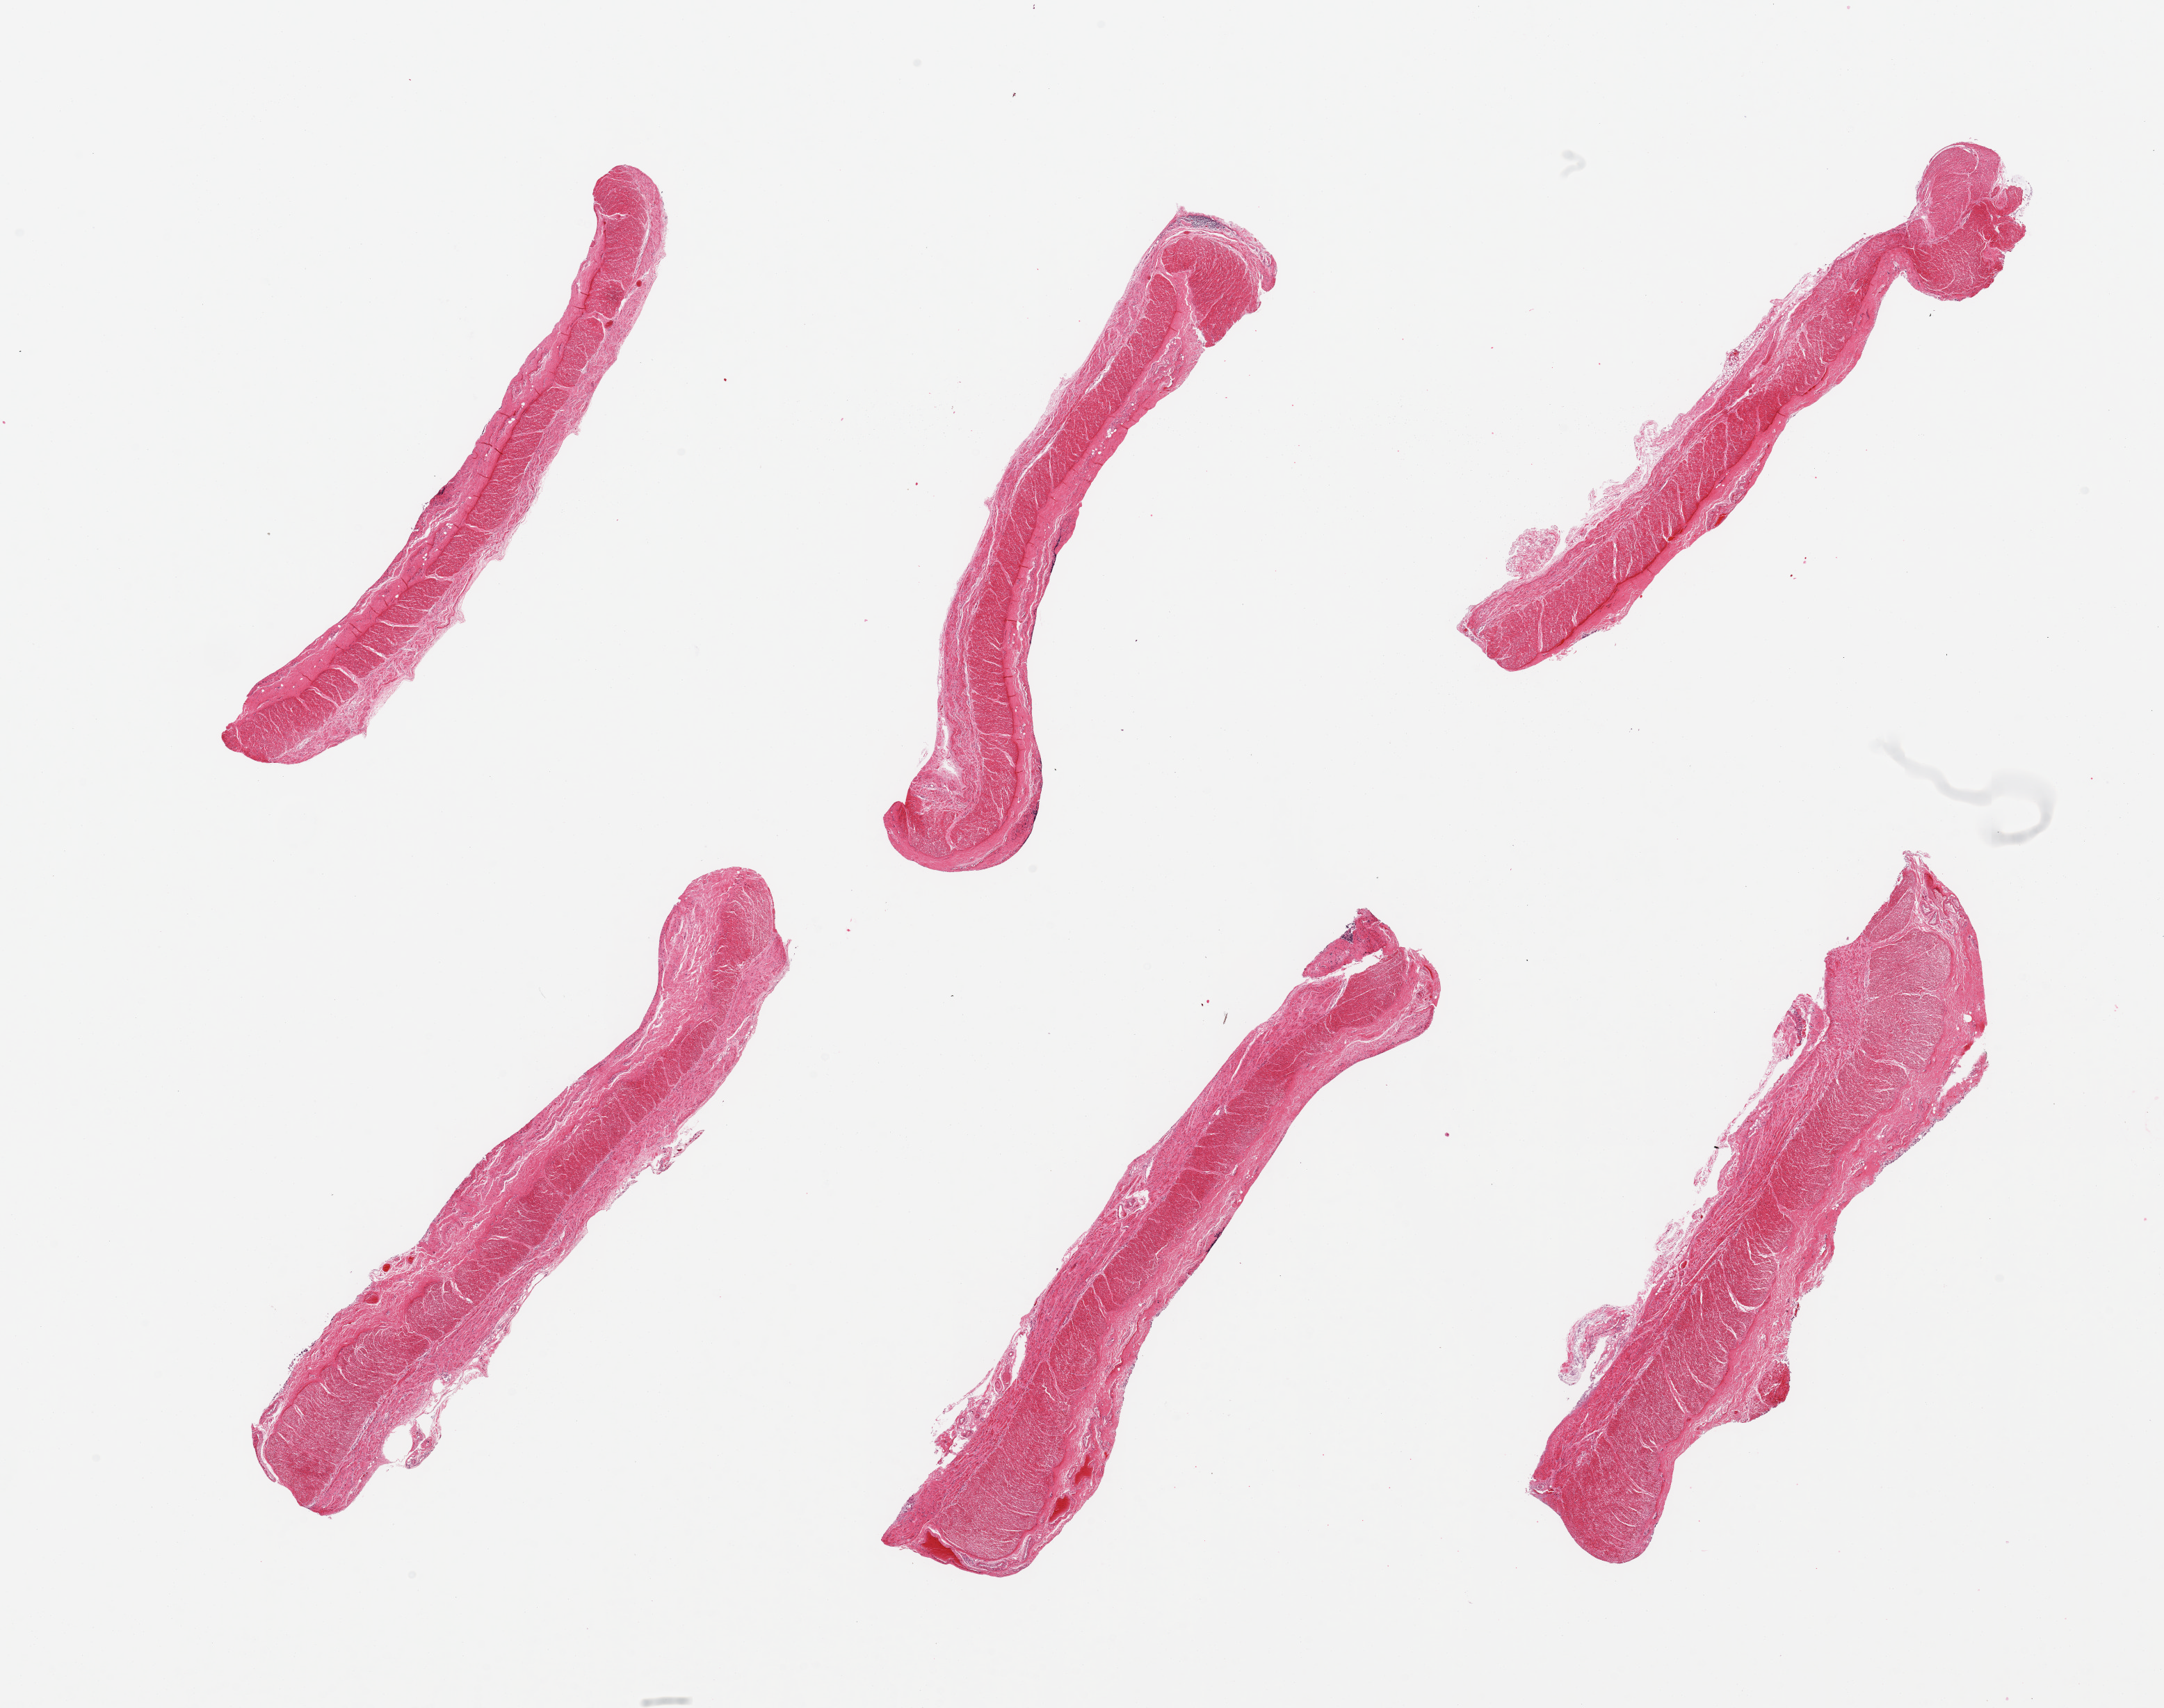
Hematoxylin and eosin (H&E) whole-slide image, a low-resolution overview of the entire scanned area, about 24.6 x 19.4 mm (from a 20x scan); PAXgene-fixed paraffin-embedded (PFPE) section; target tissue: sigmoid colon; donor tissue sample. Donor sex: male.
• review note (as recorded): 6 pieces; target muscularis with over 0.5mm congested submucosa